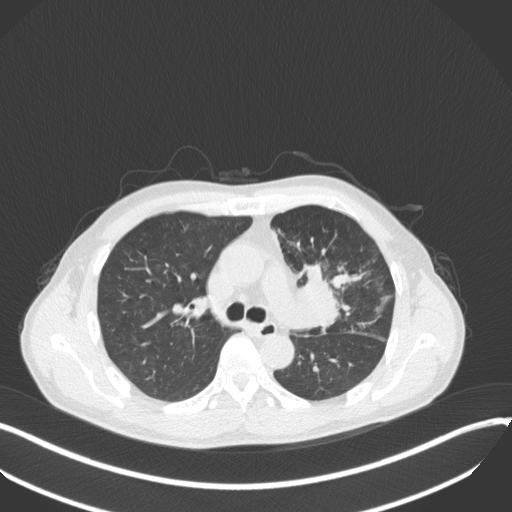
Chest CT, one axial slice. Slice 219 of 411 in the series (ordered by position). Lung window (W 1500 / L -600 HU). 512 × 512 image matrix, field of view 400 × 400 mm. Male patient, age 56 years. From the clinical record (not read from this slice): clinical TNM (as recorded): T2a N0 M0.
Annotated regions visible in this slice (rectangle marked by the reading radiologist):
- lung tumour (recorded histology: squamous cell carcinoma): bounding box [x1, y1, x2, y2] px = [292, 260, 347, 332]